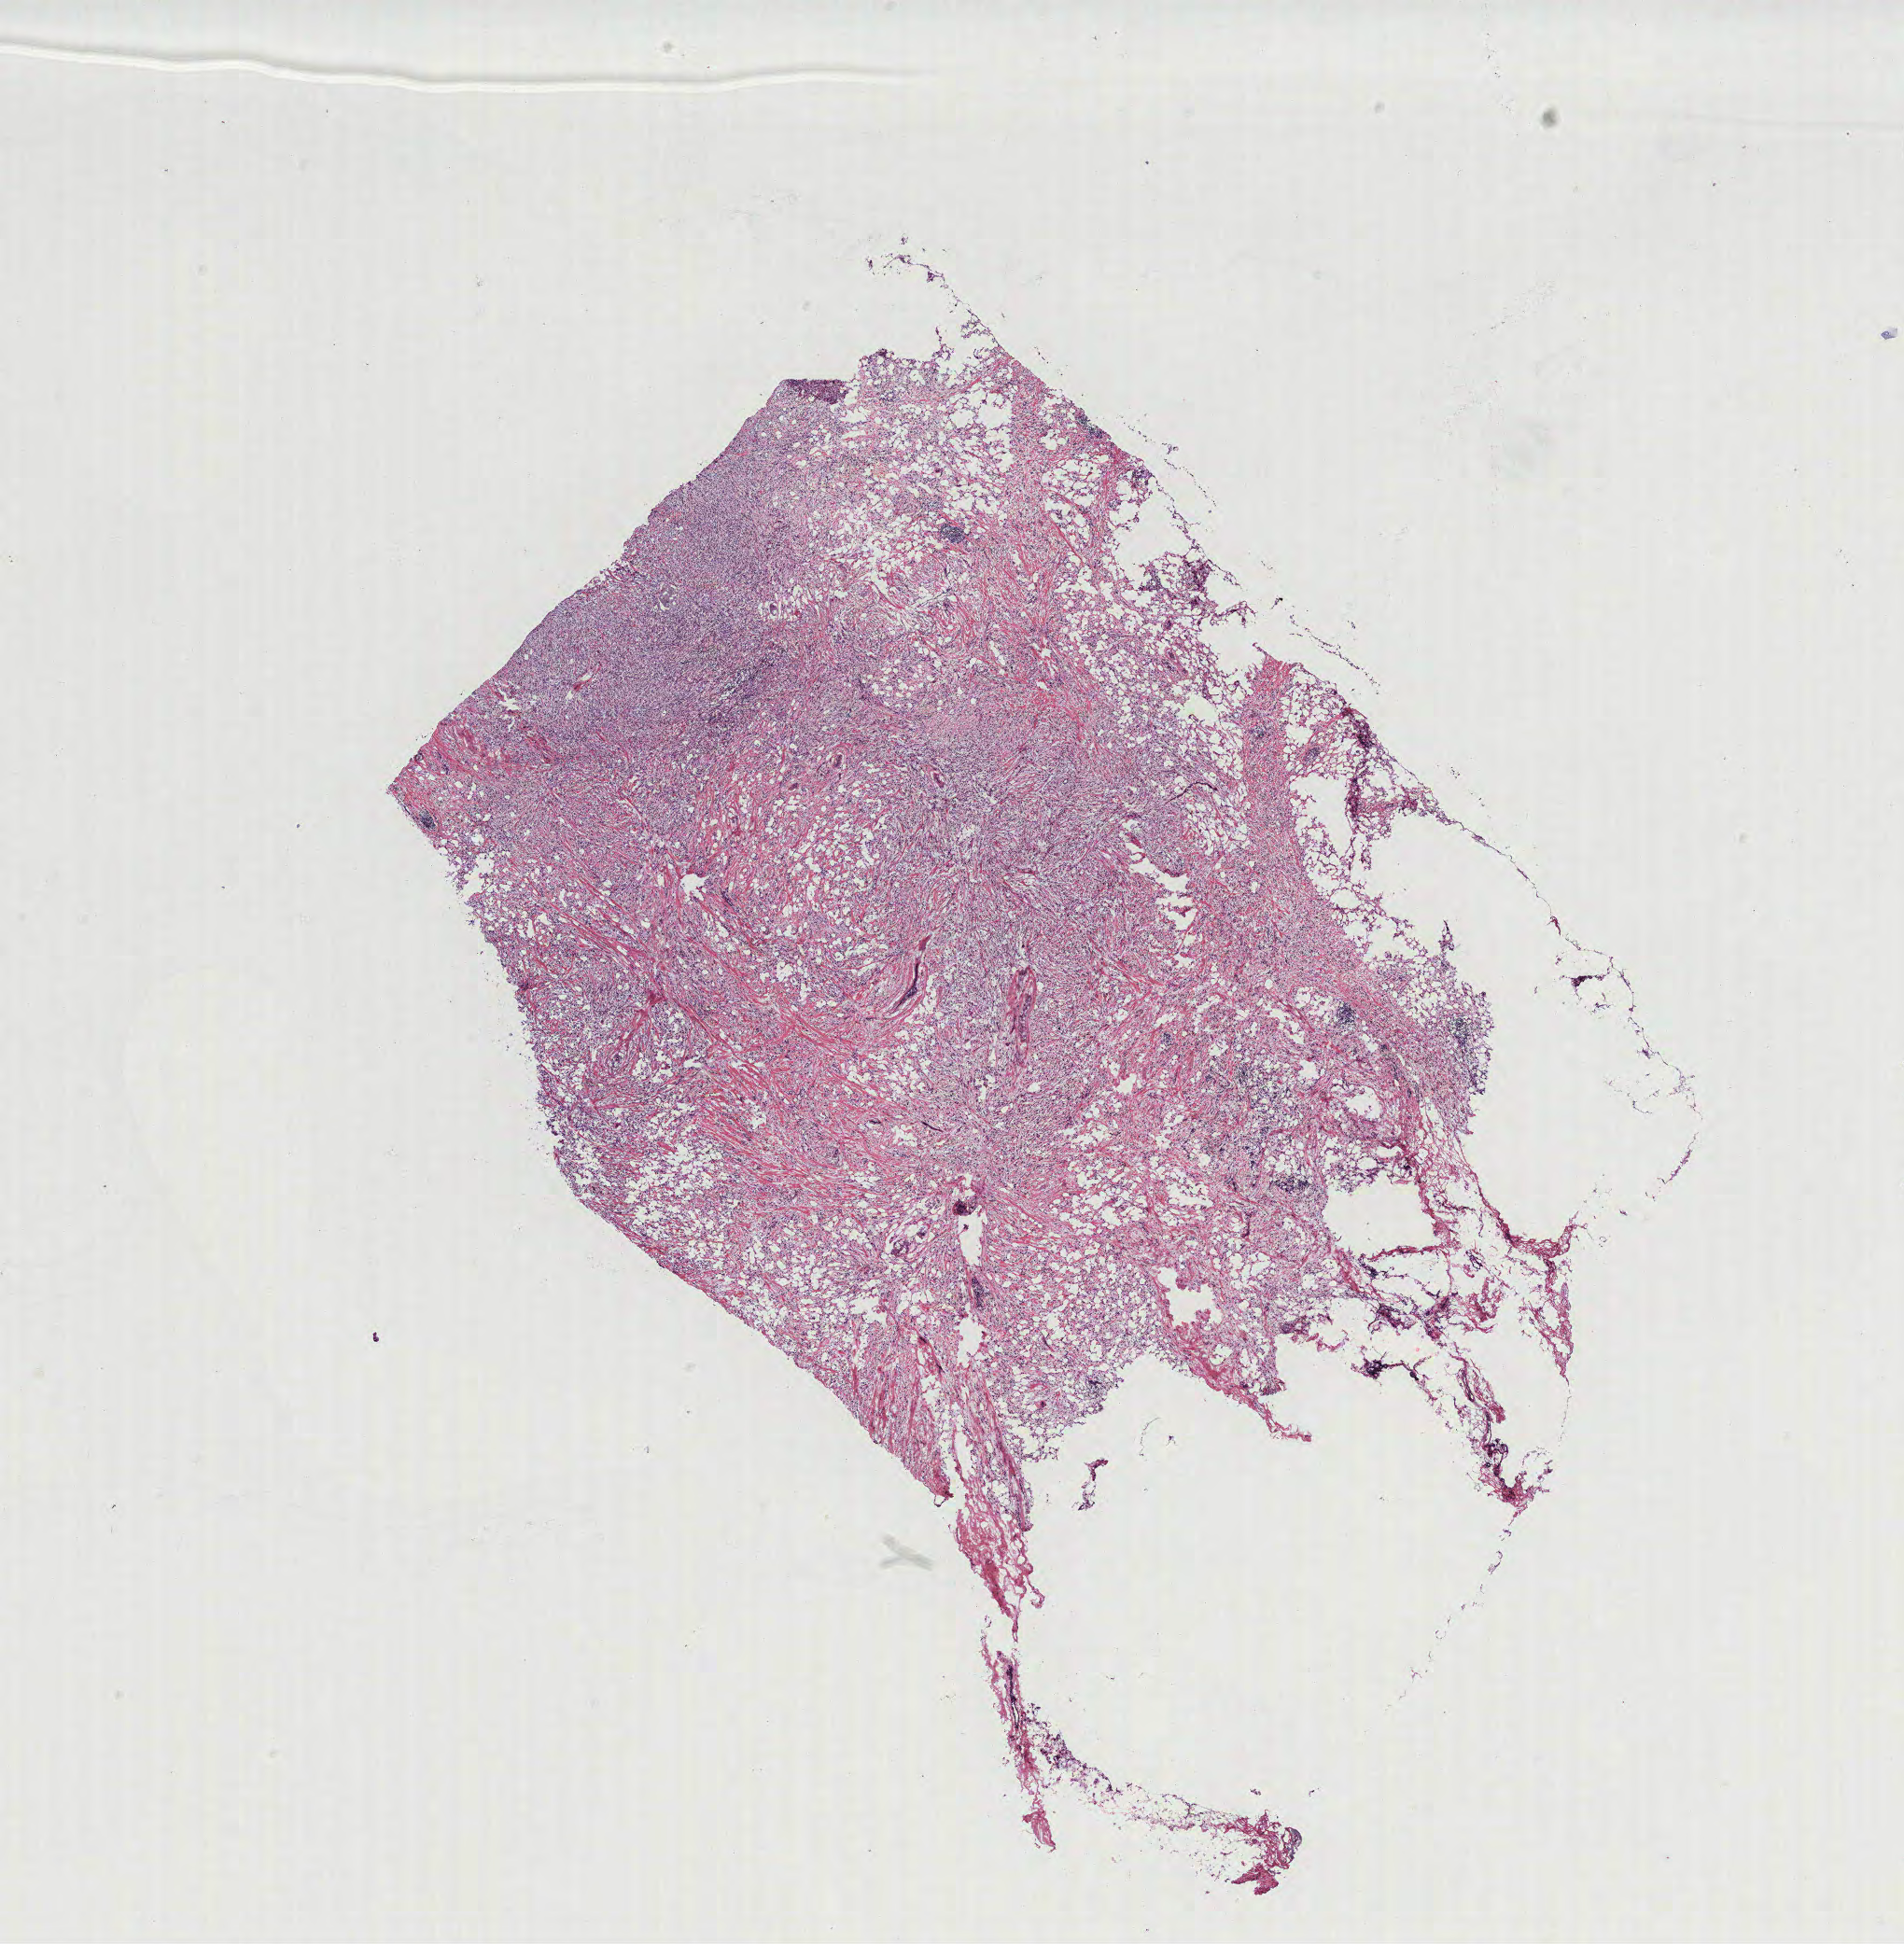
H&E whole-slide image — whole scanned area (about 16.3 x 16.7 mm, acquisition: 40x scan) shown as a low-resolution overview, breast, tissue type not recorded. Female patient.
Patient diagnosis: Infiltrating duct carcinoma, NOS.